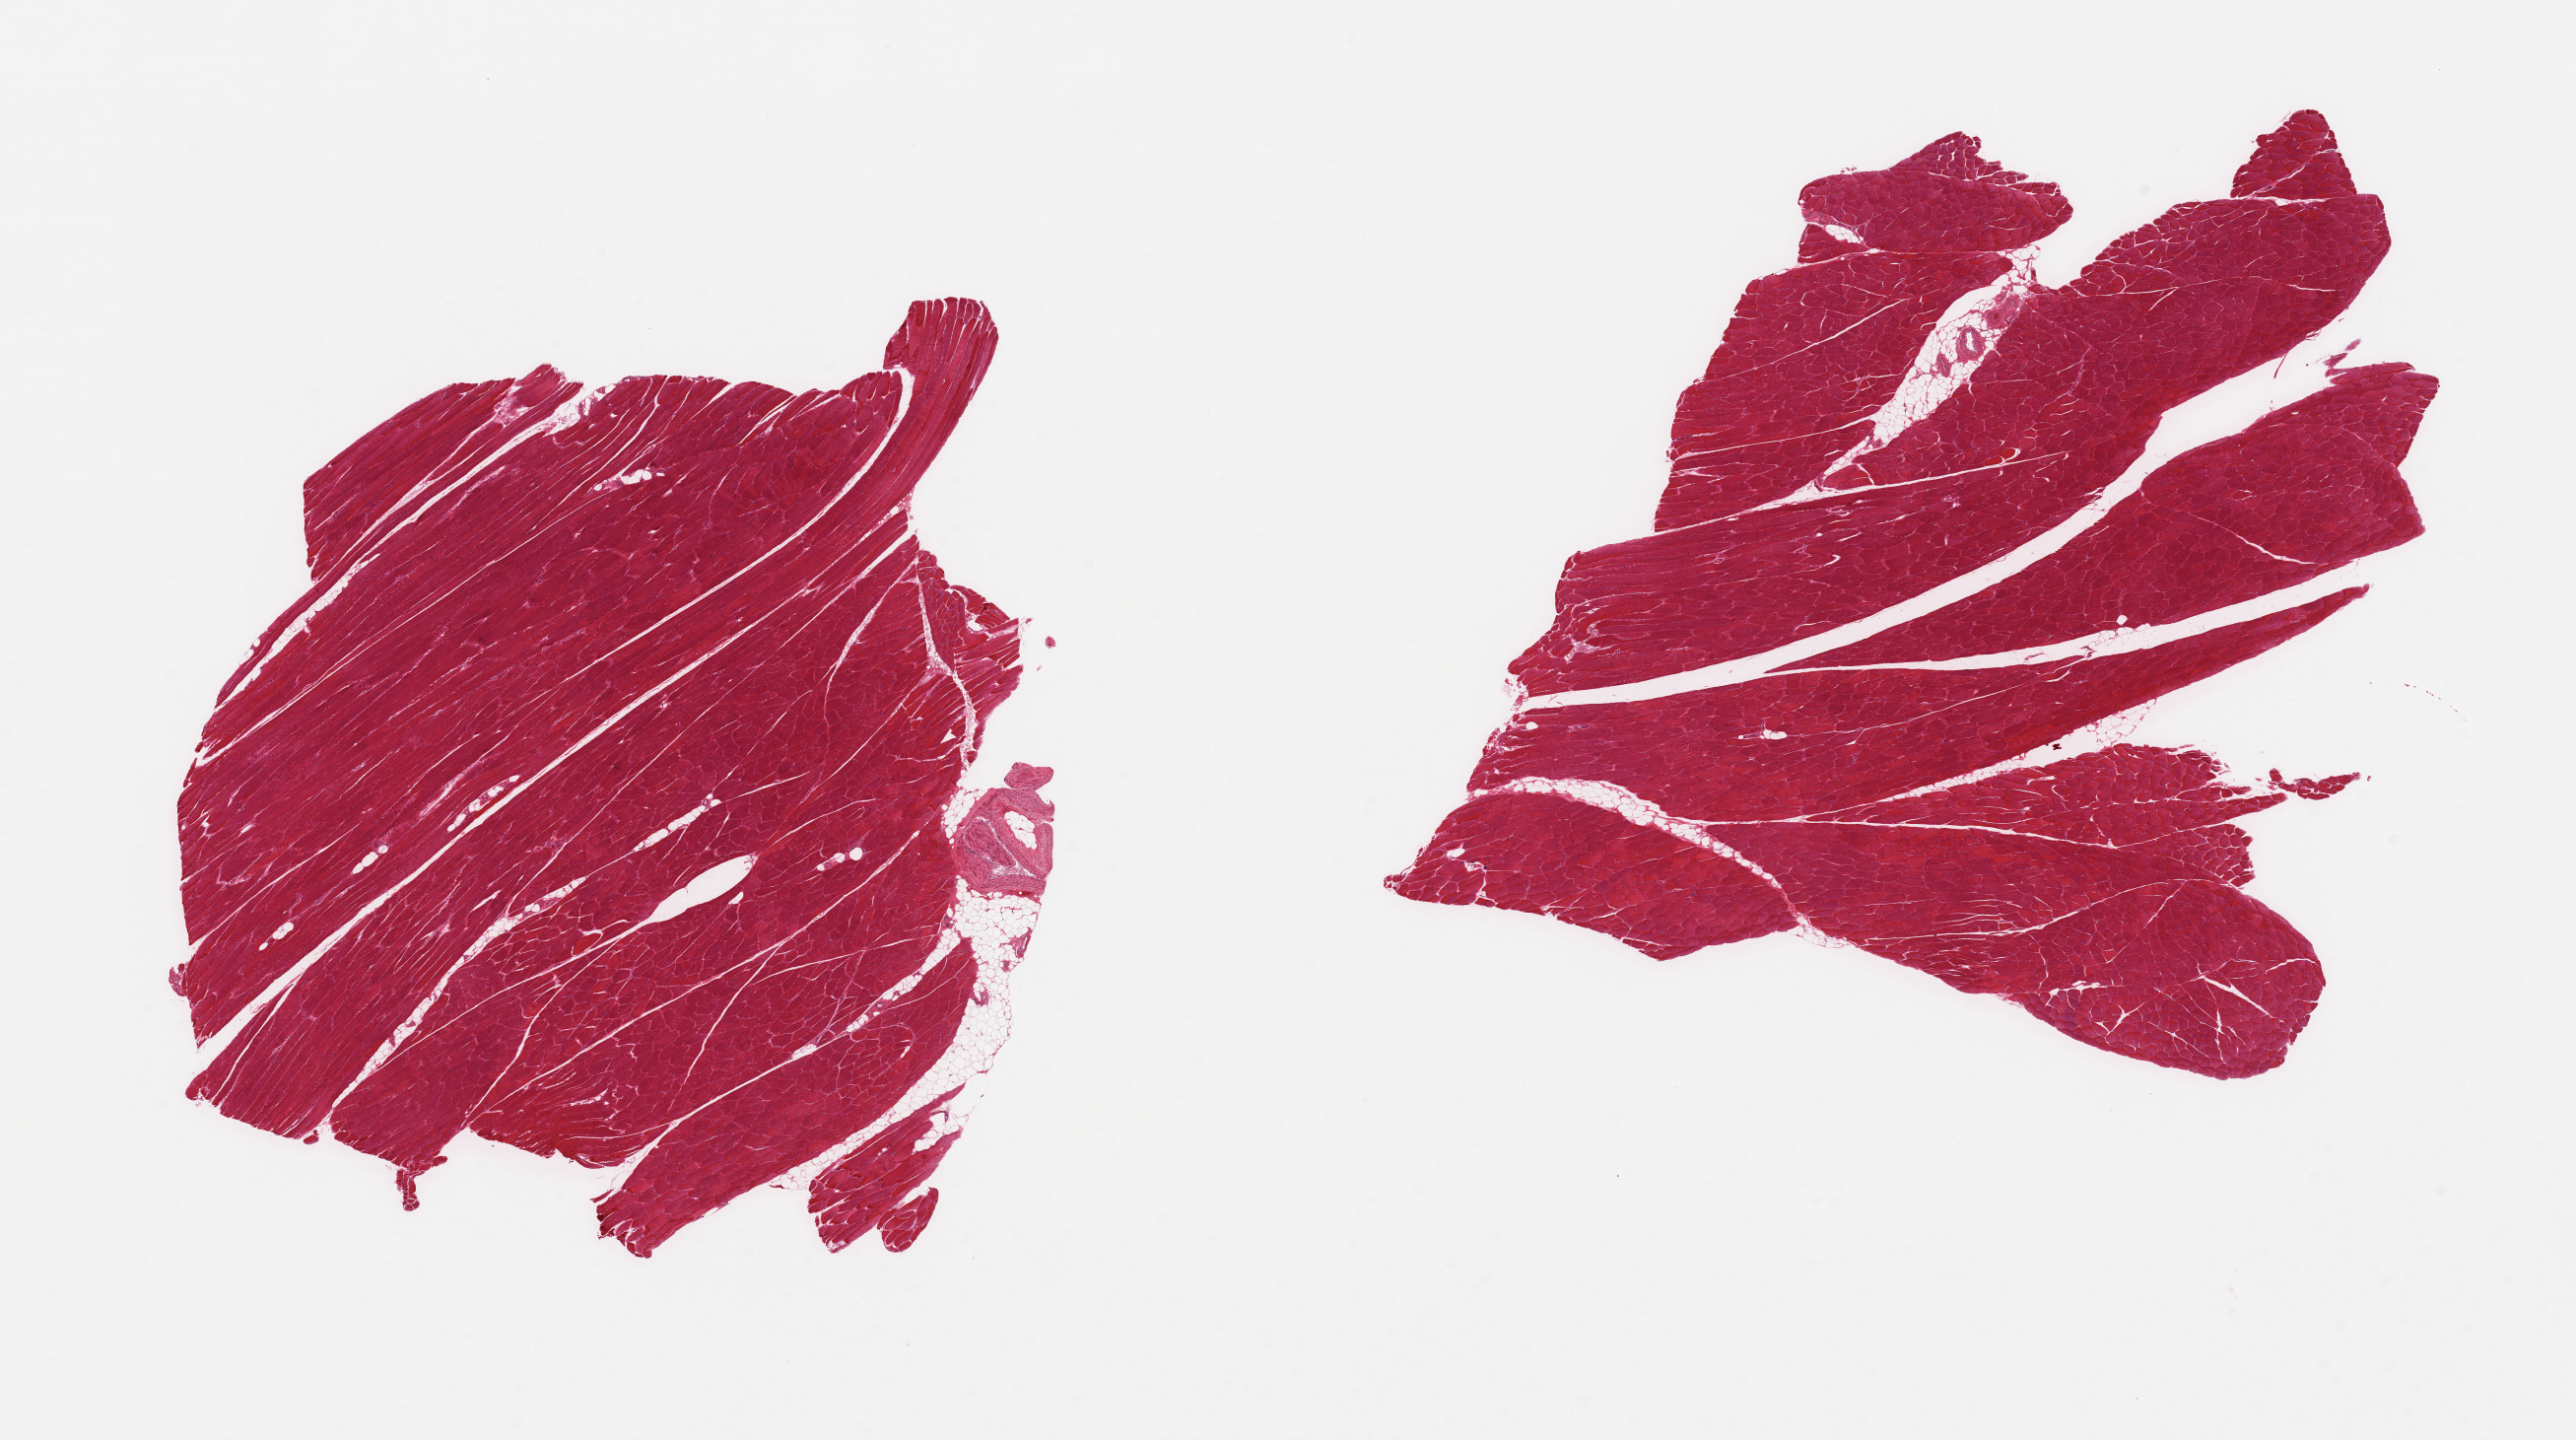
H&E whole-slide image — shown as a low-resolution overview of the whole scanned area (about 20.7 x 11.6 mm, acquisition: 20x scan); PAXgene-fixed, paraffin-embedded tissue; sampled site (target tissue): skeletal muscle; donor tissue sample. Donor: female.
Reviewer comment on this tissue sample: 2 pieces, 10 -15% interstitial fat.